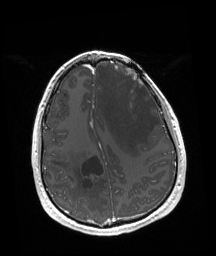
Brain MRI from a brain-tumour surgery series, one axial slice; position 58 of 192 along the scan axis; T1-weighted post-contrast; 1 mm slice thickness; 216 × 256 image matrix.
Annotated regions visible in this slice (outlined manually by an expert reader):
- tumour: bounding box (x1, y1, x2, y2) in pixels: (124, 67, 142, 86)